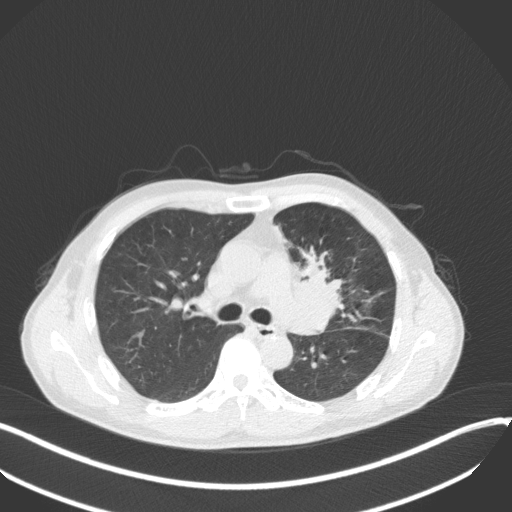
Chest CT, one axial slice. Slice 212 of 411 in the series (ordered by position). Reconstruction kernel B31f. 120 kVp. Lung window (W 1500 / L -600 HU). 512 × 512 image matrix. Patient: male, 56 years. Case-level facts recorded for this patient, not image findings: clinical TNM (as recorded): T2a N0 M0.
Annotated regions visible in this slice (rectangle marked by the reading radiologist):
- lung tumour (recorded histology: squamous cell carcinoma): box from (x=291, y=250) to (x=348, y=333) px